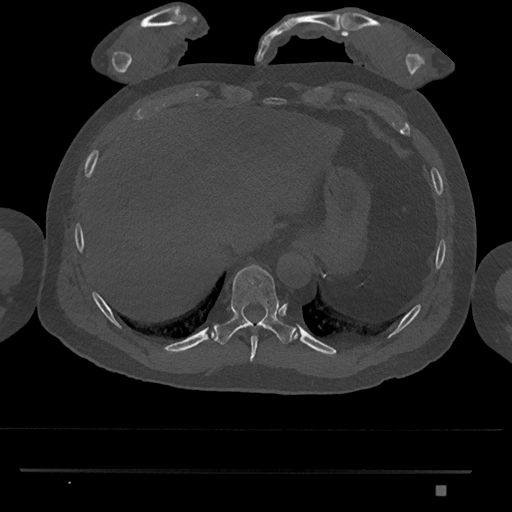
CT including the spine, one axial slice; slice 1013 of 1134 in the series (ordered by position); 120 kVp; bone window (W 1800 / L 400 HU); 0.5 mm slice thickness; 512 × 512 image matrix. Male patient, age 65 years. Case-level facts recorded for this patient, not image findings: primary cancer: prostate.
Outlined on this slice (semi-automatic segmentation, software-assisted and operator-edited):
- T10 vertebra: box from (x=213, y=264) to (x=294, y=345) px
- T9 vertebra: (x=250, y=335)–(x=258, y=362)